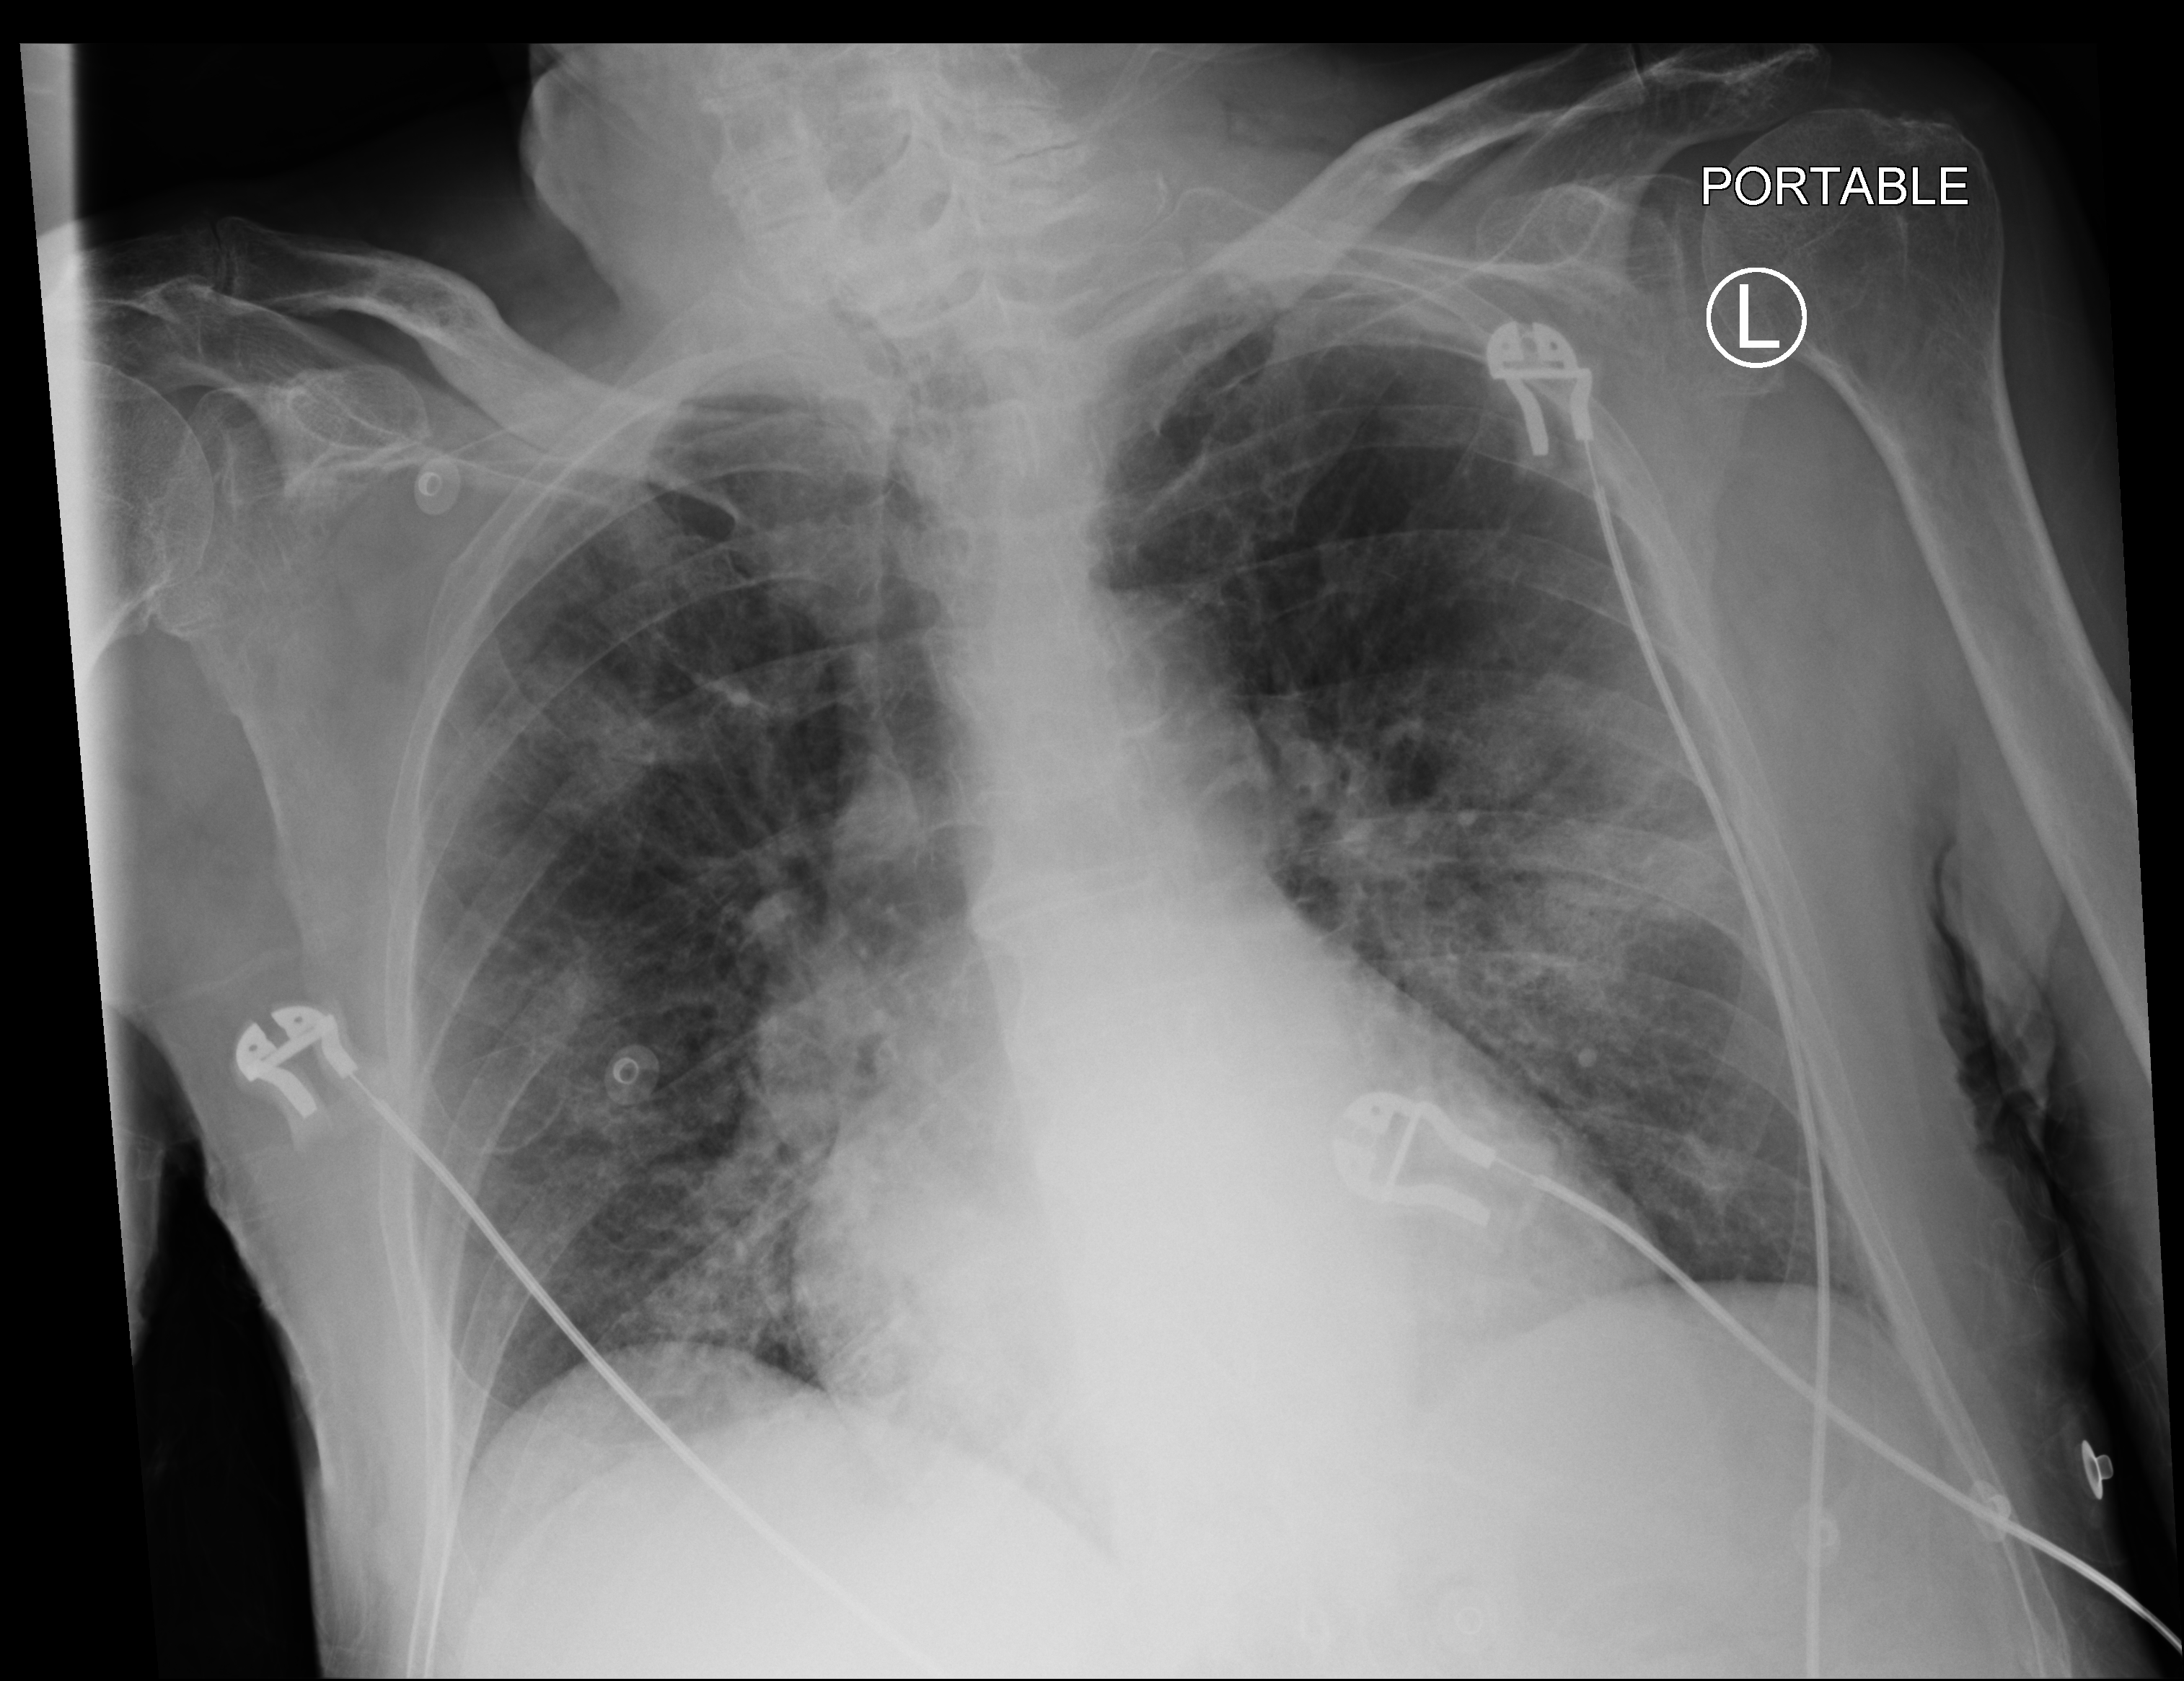
Chest X-ray (portable); anteroposterior (AP) projection. Male patient hospitalised with COVID-19, age 75–90 years.
Hospital-stay facts (about this admission, not read from this image; timing relative to this image not recorded): hypertension (admission record): yes.